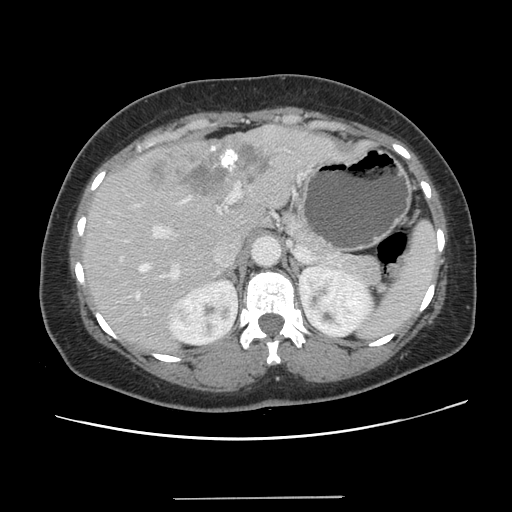
Contrast-enhanced abdominal CT, one axial slice; position 87 of 141 along the scan axis; 120 kVp; intravenous contrast given; soft-tissue window (W 400 / L 40 HU); 2.5 mm slice thickness; 512 × 512 image matrix. Female patient, age 53 years. Case-level facts recorded for this patient, not image findings: diagnosis: colorectal cancer liver metastases, imaged before liver resection; multiple liver metastases: no; largest metastasis: 14.5 cm; disease in both lobes: yes.
Annotated regions visible in this slice (manually delineated by an expert):
- hepatic veins: box from (x=136, y=199) to (x=187, y=298) px
- liver: (x=83, y=126)–(x=368, y=352)
- planned liver remnant (the part of the liver to remain after resection): (x=83, y=207)–(x=264, y=352)
- portal vein (with intrahepatic branches): (x=152, y=184)–(x=240, y=282)
- liver metastasis: (x=152, y=141)–(x=273, y=195)